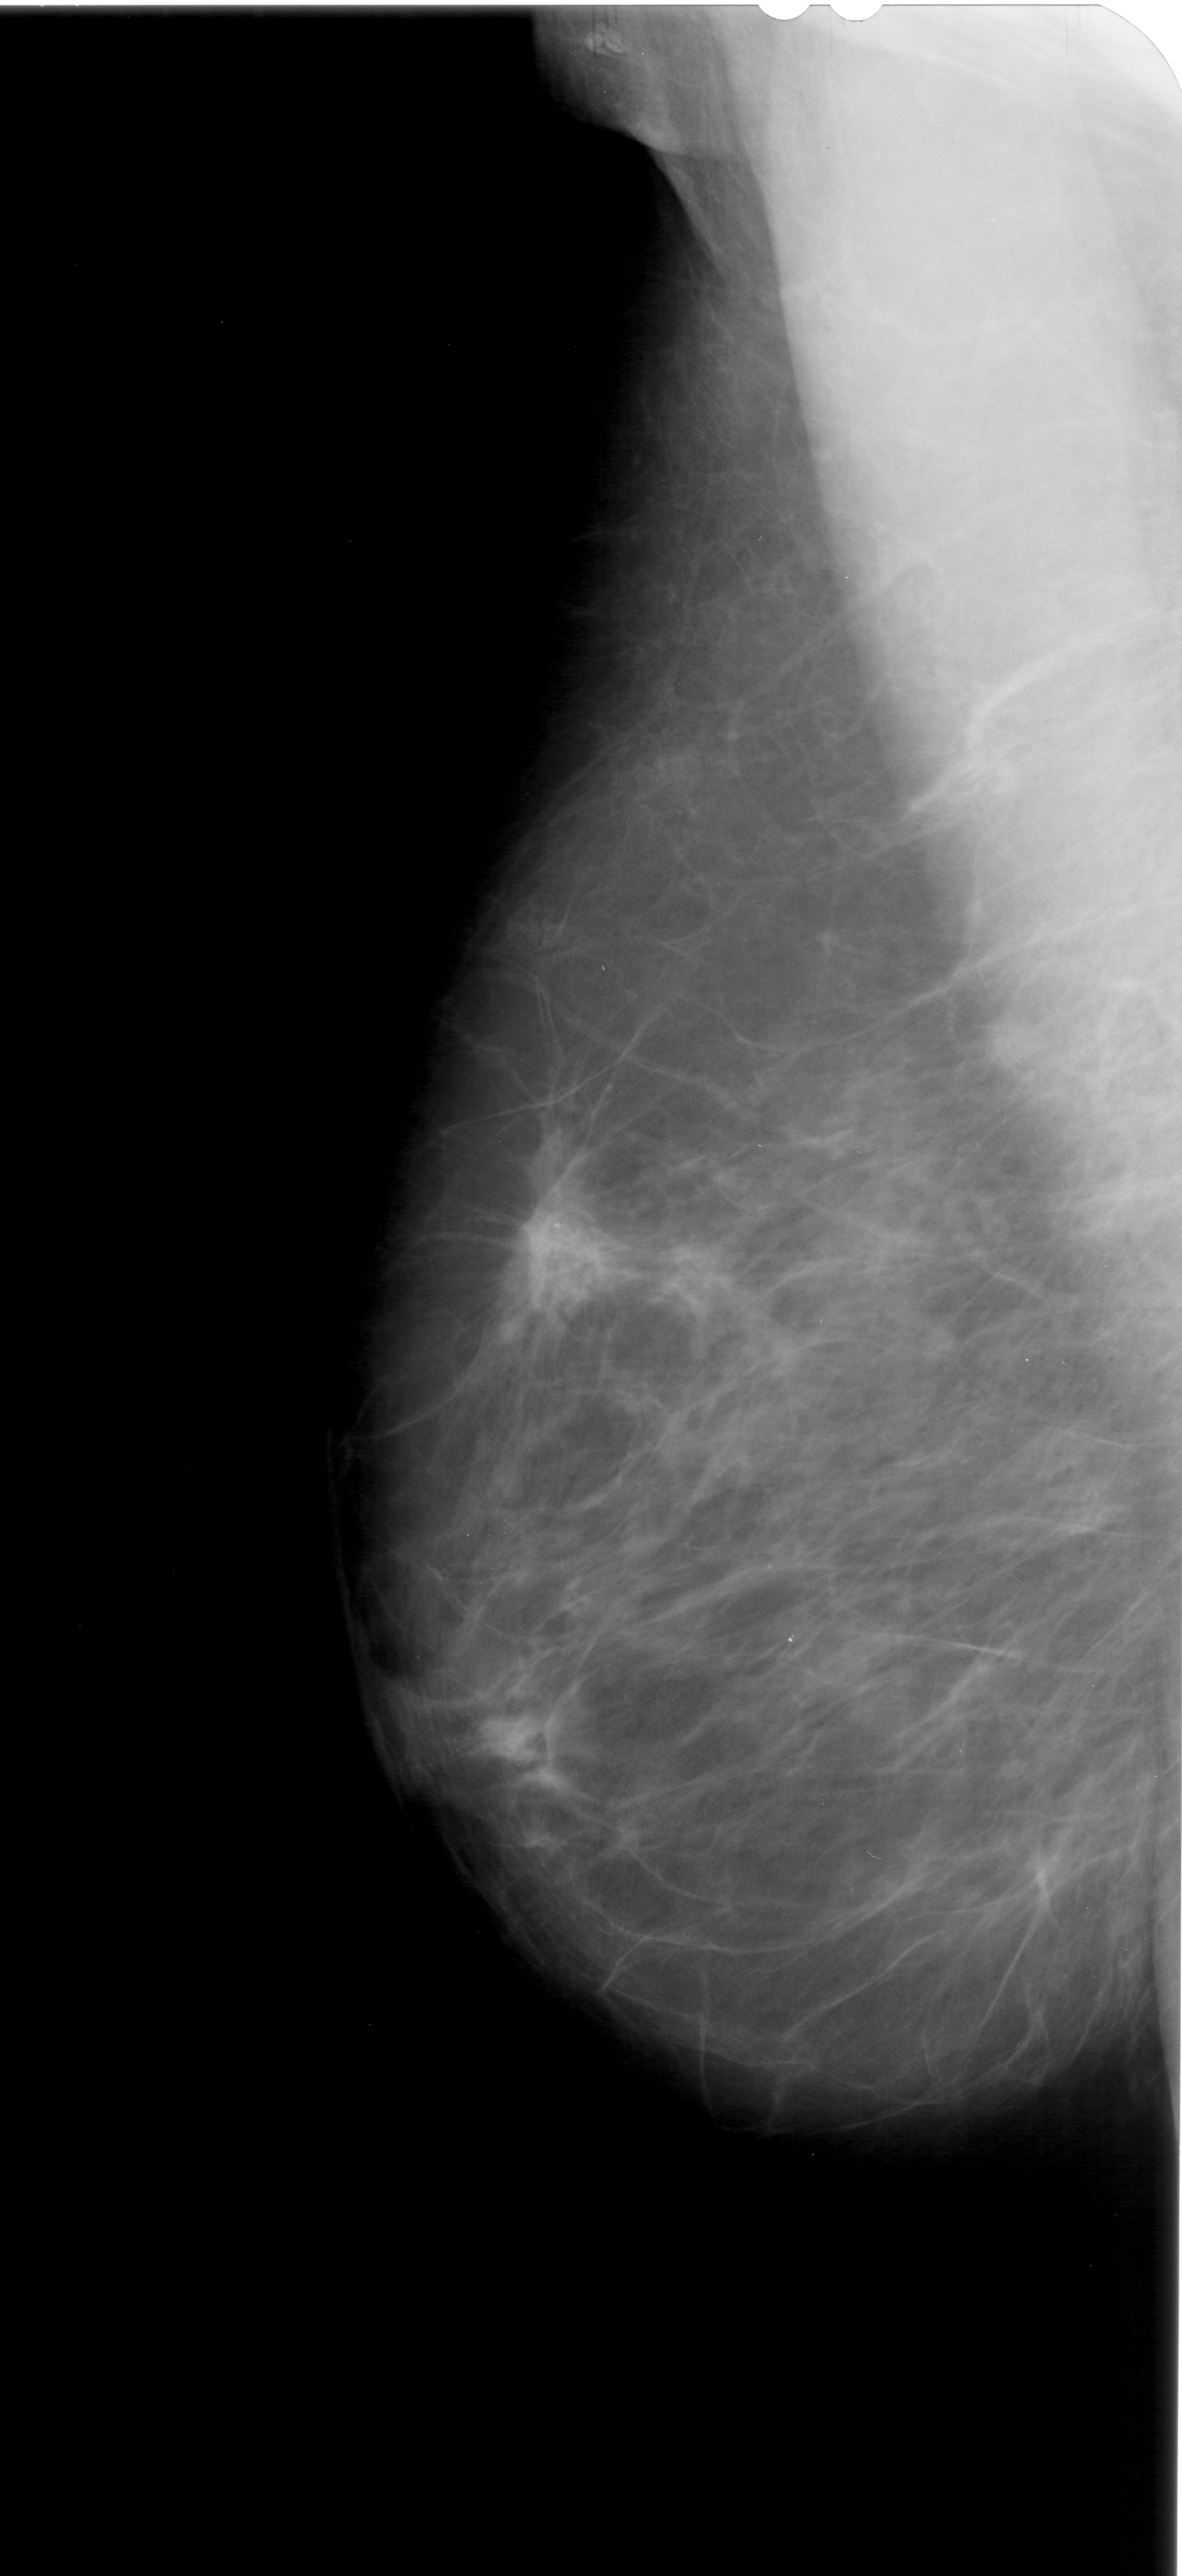
Scanned film-screen mammogram, left breast, mediolateral oblique (MLO) view.
Mass, shape irregular, margins spiculated; BI-RADS assessment category 5; pathology (as recorded): malignant.